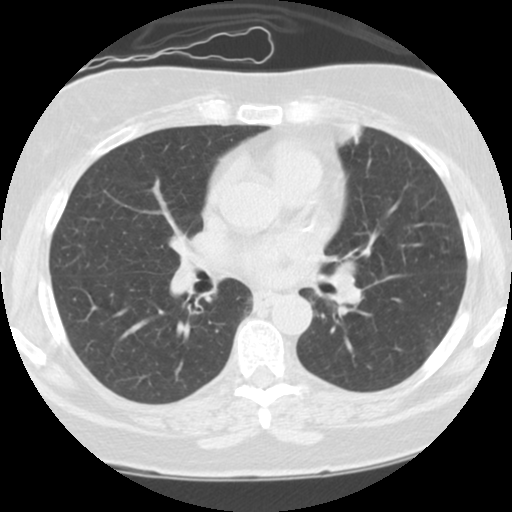
Chest CT (low-dose screening protocol), one axial image; third annual screen; lung window (W 1500 / L -600 HU); 2.5 mm slice thickness; slice 50 of 108 in the series; 512 × 512 image matrix. Female participant, aged 59 years at enrolment.
Expert reader's lesion annotation, bounding box (x1, y1, x2, y2) in pixels: (285, 213, 392, 326). No non-calcified nodule or mass ≥4 mm was recorded by the screening reader at this exam.